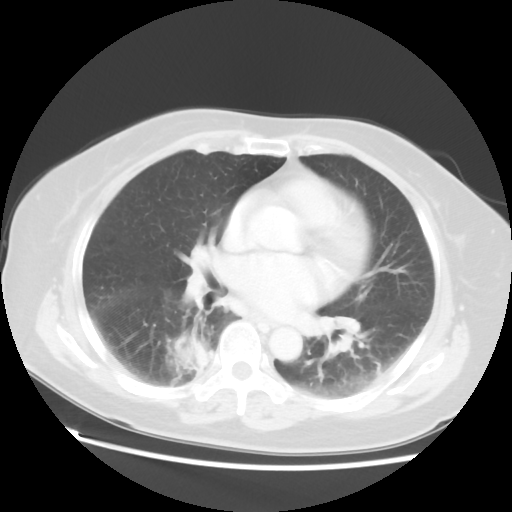
Chest CT, one axial slice. Slice 28 of 52 in the series (ordered by position). Reconstruction kernel STANDARD. Lung window (W 1500 / L -600 HU). 512 × 512 image matrix, field of view 356 × 356 mm. Patient: female, 69 years. Case-level facts recorded for this patient, not image findings: clinical TNM (as recorded): T2 N1 M1a.
Structures marked on this image (rectangle marked by the reading radiologist):
- lung tumour (recorded histology: adenocarcinoma): bounding box <169,329,210,382> (left, top, right, bottom; pixels)